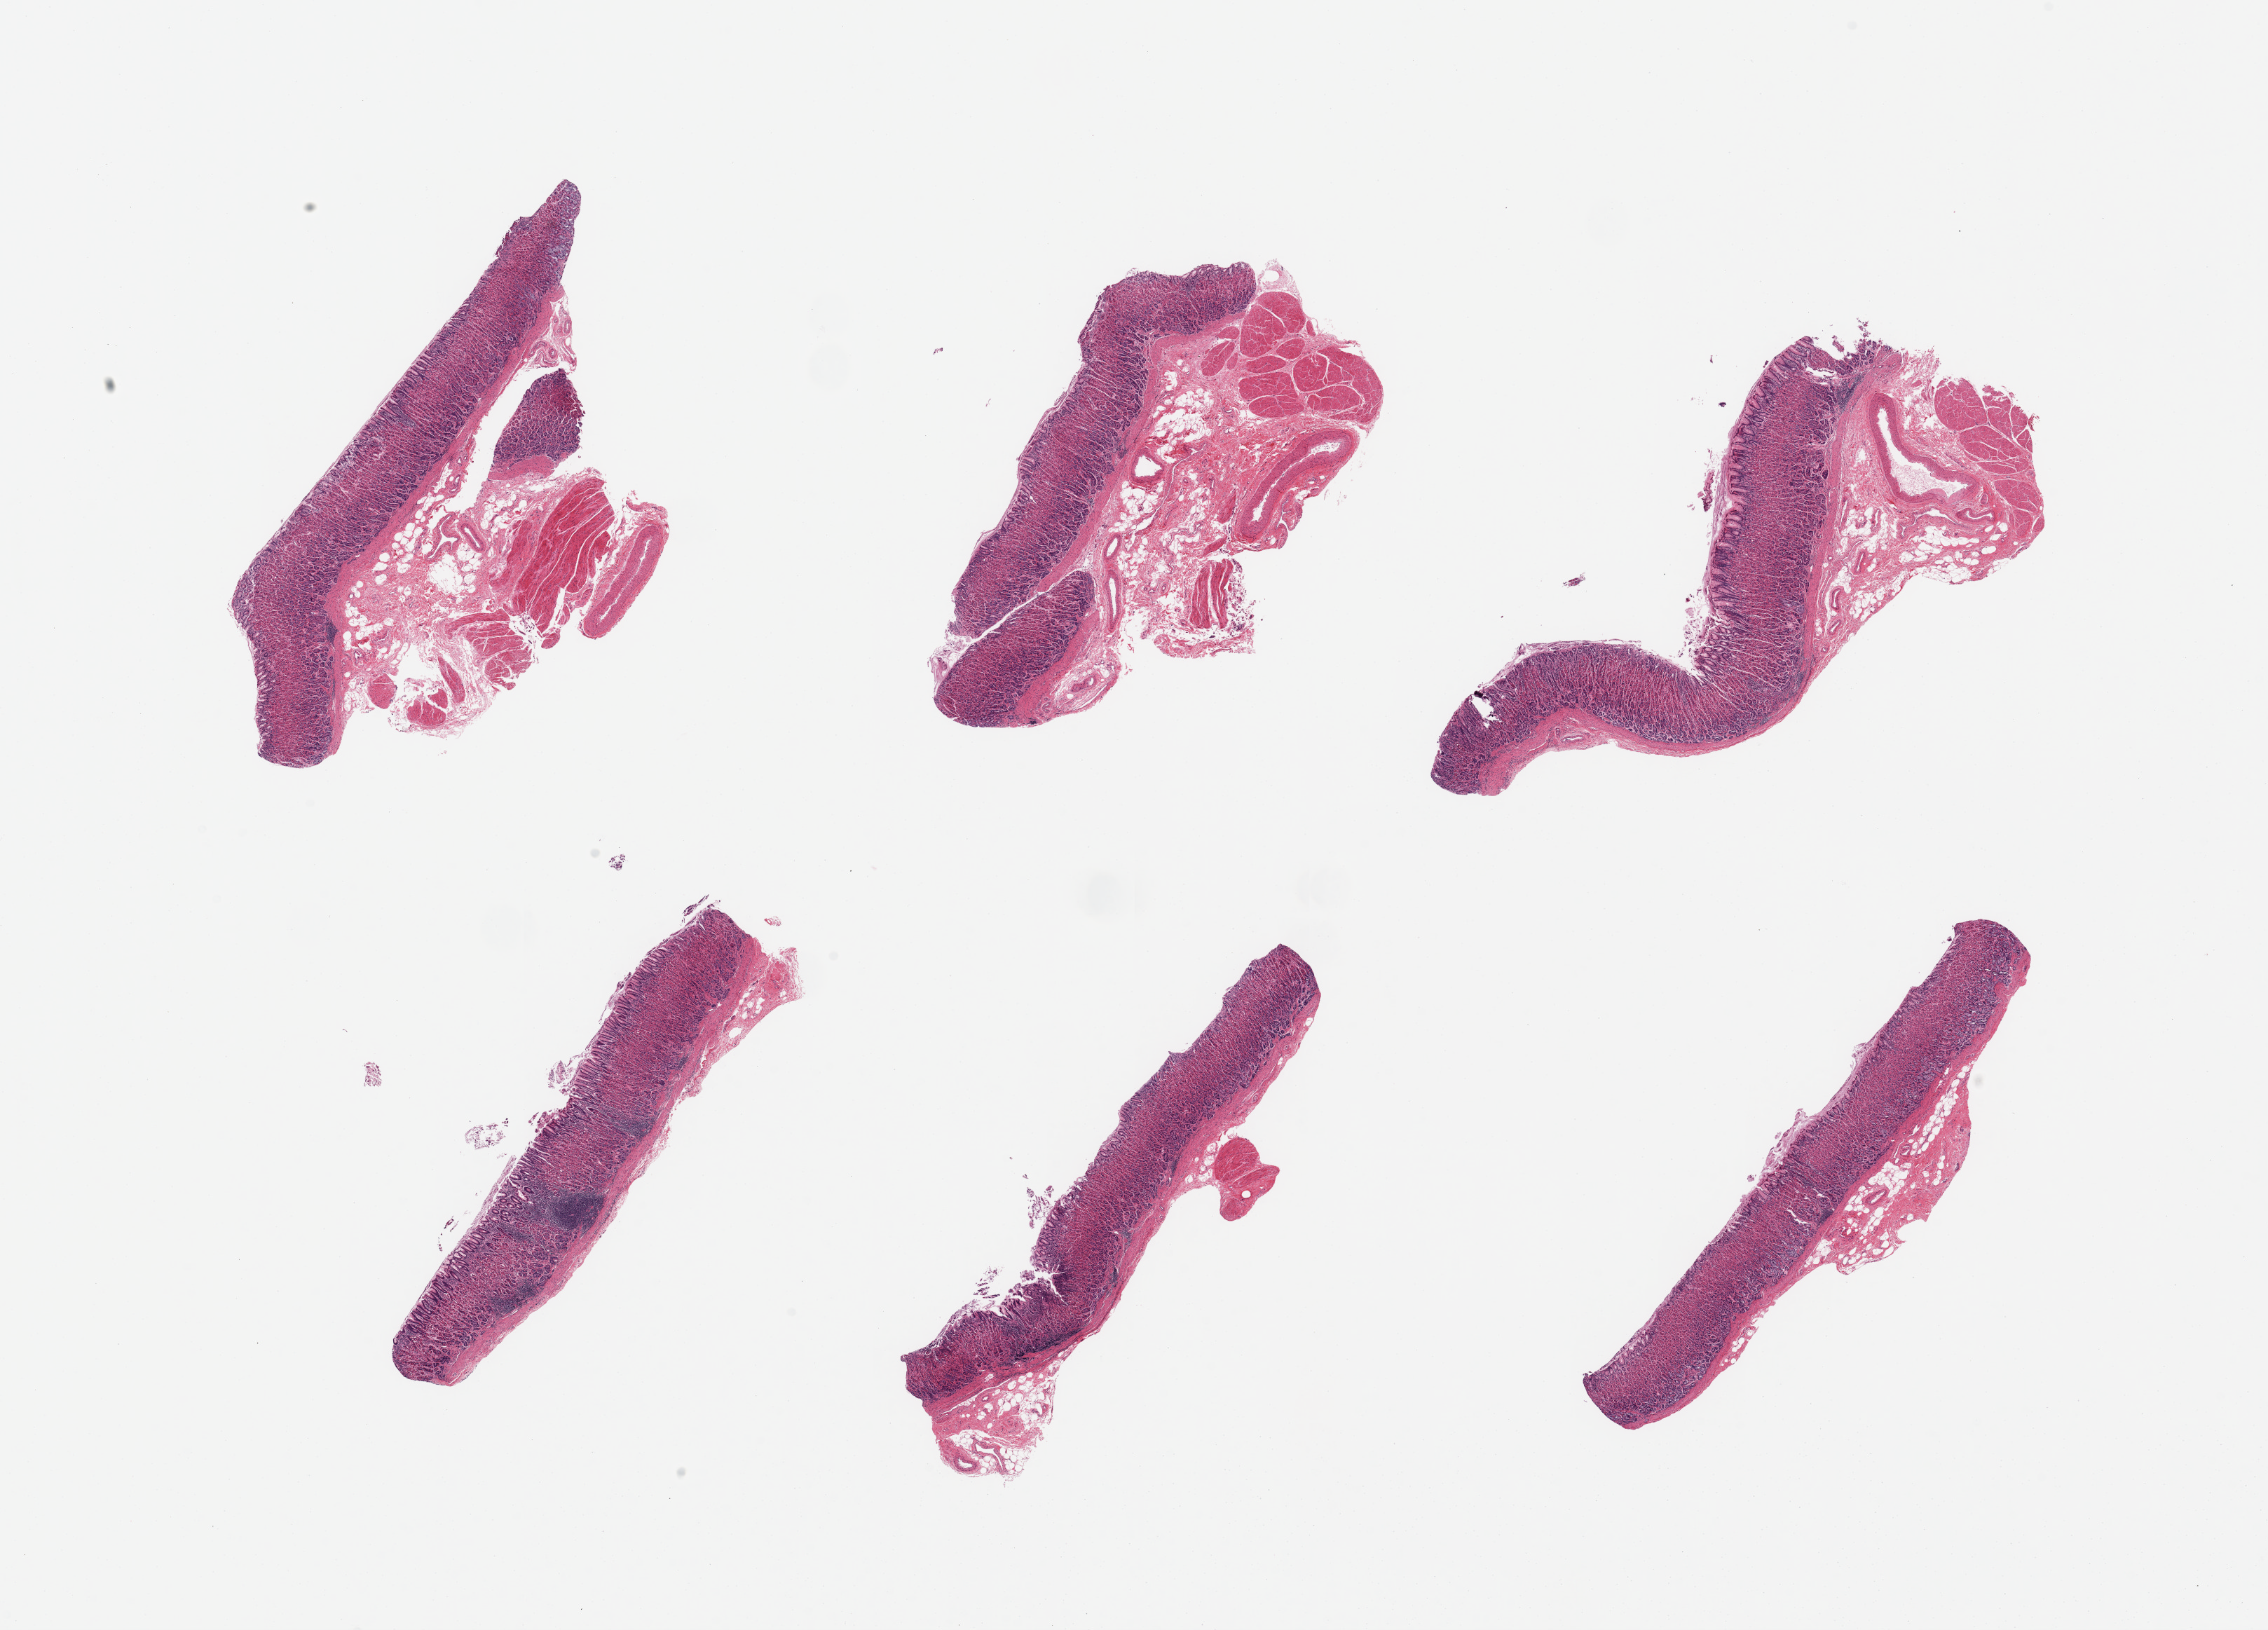
Whole-slide image, hematoxylin and eosin (H&E) stain, brightfield — a low-resolution overview of the entire scanned area, about 25.6 x 18.4 mm. PAXgene-fixed, paraffin-embedded tissue. Section of stomach (target tissue). Donor tissue sample. Donor sex: female.
Pathologist's review note for this sample: 6 pieces; chronic gastritis; no muscle on 3 pieces.